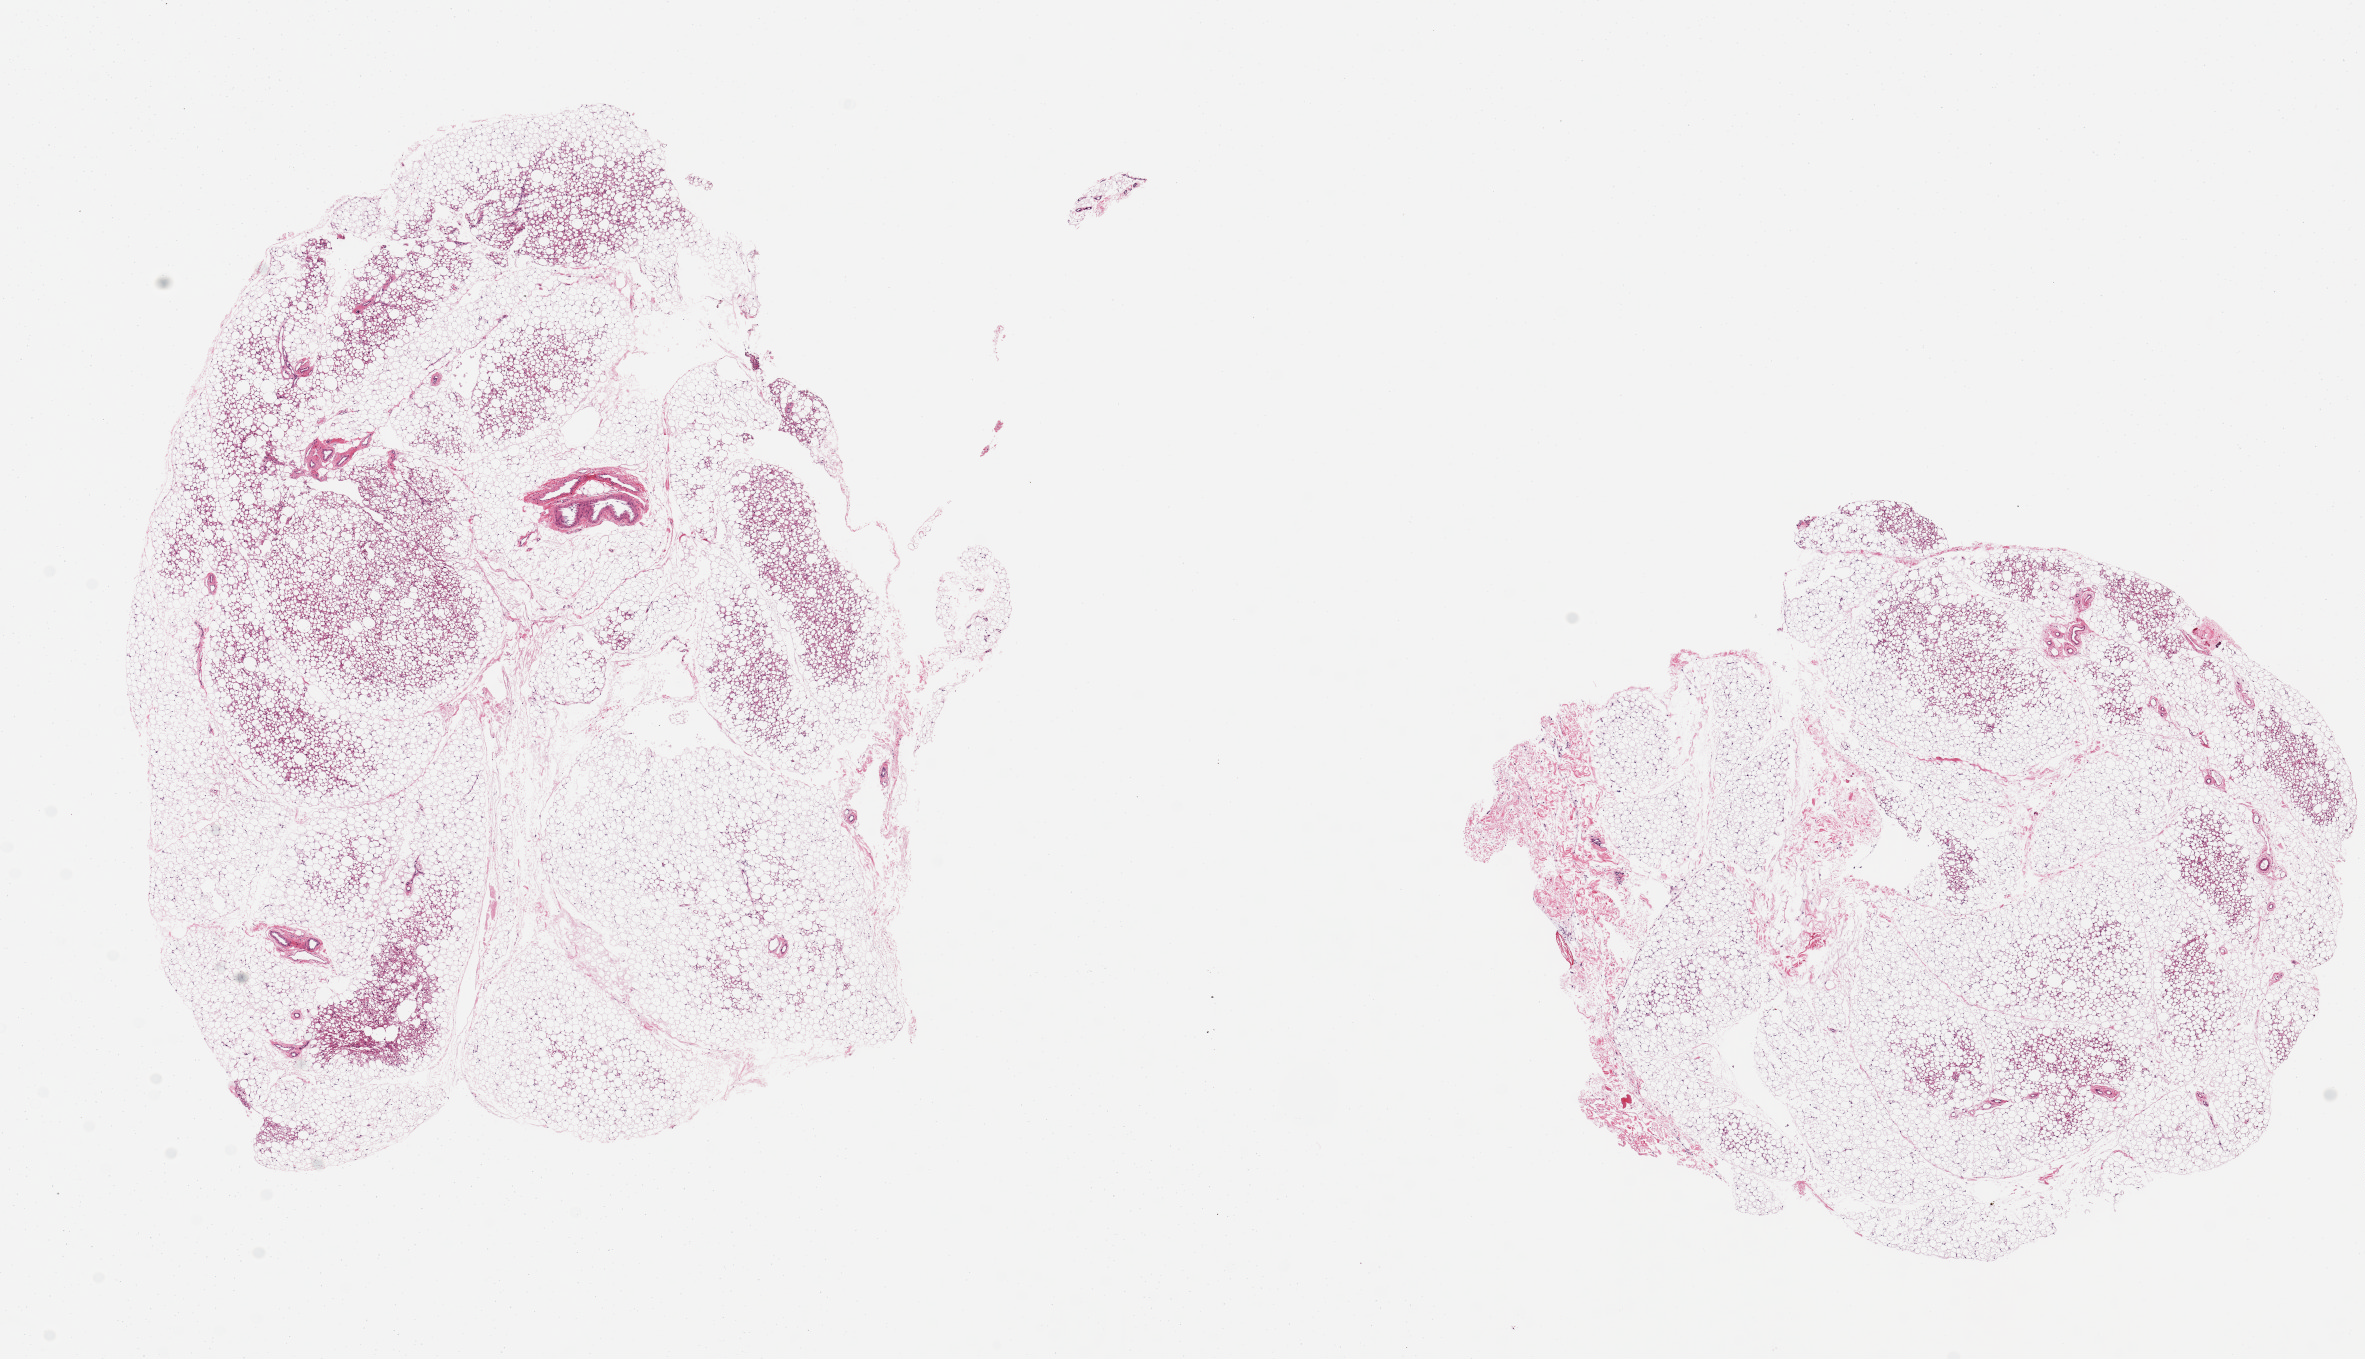
Whole-slide image, haematoxylin and eosin stain, brightfield — a low-resolution overview of the entire scanned area, about 18.7 x 10.7 mm (acquisition: 20x scan). PAXgene-fixed, paraffin-embedded tissue. Sampled site (target tissue): adrenal gland. Tissue donor sample. Donor sex: female.
Reviewer comment on this tissue sample: 2 pieces, ~8x7mm. No adrenal; all fat.